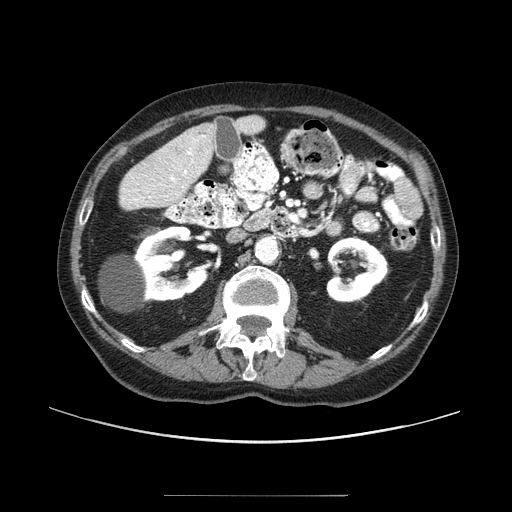
Contrast-enhanced abdominal CT (liver protocol), one axial slice. Reconstruction kernel STANDARD. One of 2 acquisitions stored at this slice position. Soft-tissue window (W 400 / L 40 HU). 2.5 mm slice thickness. 512 × 512 image matrix, field of view 400 × 400 mm. Case-level facts recorded for this patient, not image findings: diagnosis: hepatocellular carcinoma (patient treated with transarterial chemoembolisation; whether this scan precedes or follows treatment is not stated here); TNM stage (as recorded): Stage-I; Child-Pugh class: A; tumour differentiation: moderately differentiated.
Structures marked on this image (semi-automatic segmentation, software-assisted and operator-edited):
- liver parenchyma outside the tumour (the mass and vessels are separate outlines, so this box may not span the whole liver): bounding box (x1, y1, x2, y2) in pixels: (138, 122, 216, 200)
- mass: (159, 137, 190, 168)
- liver vessels: (159, 135, 205, 195)